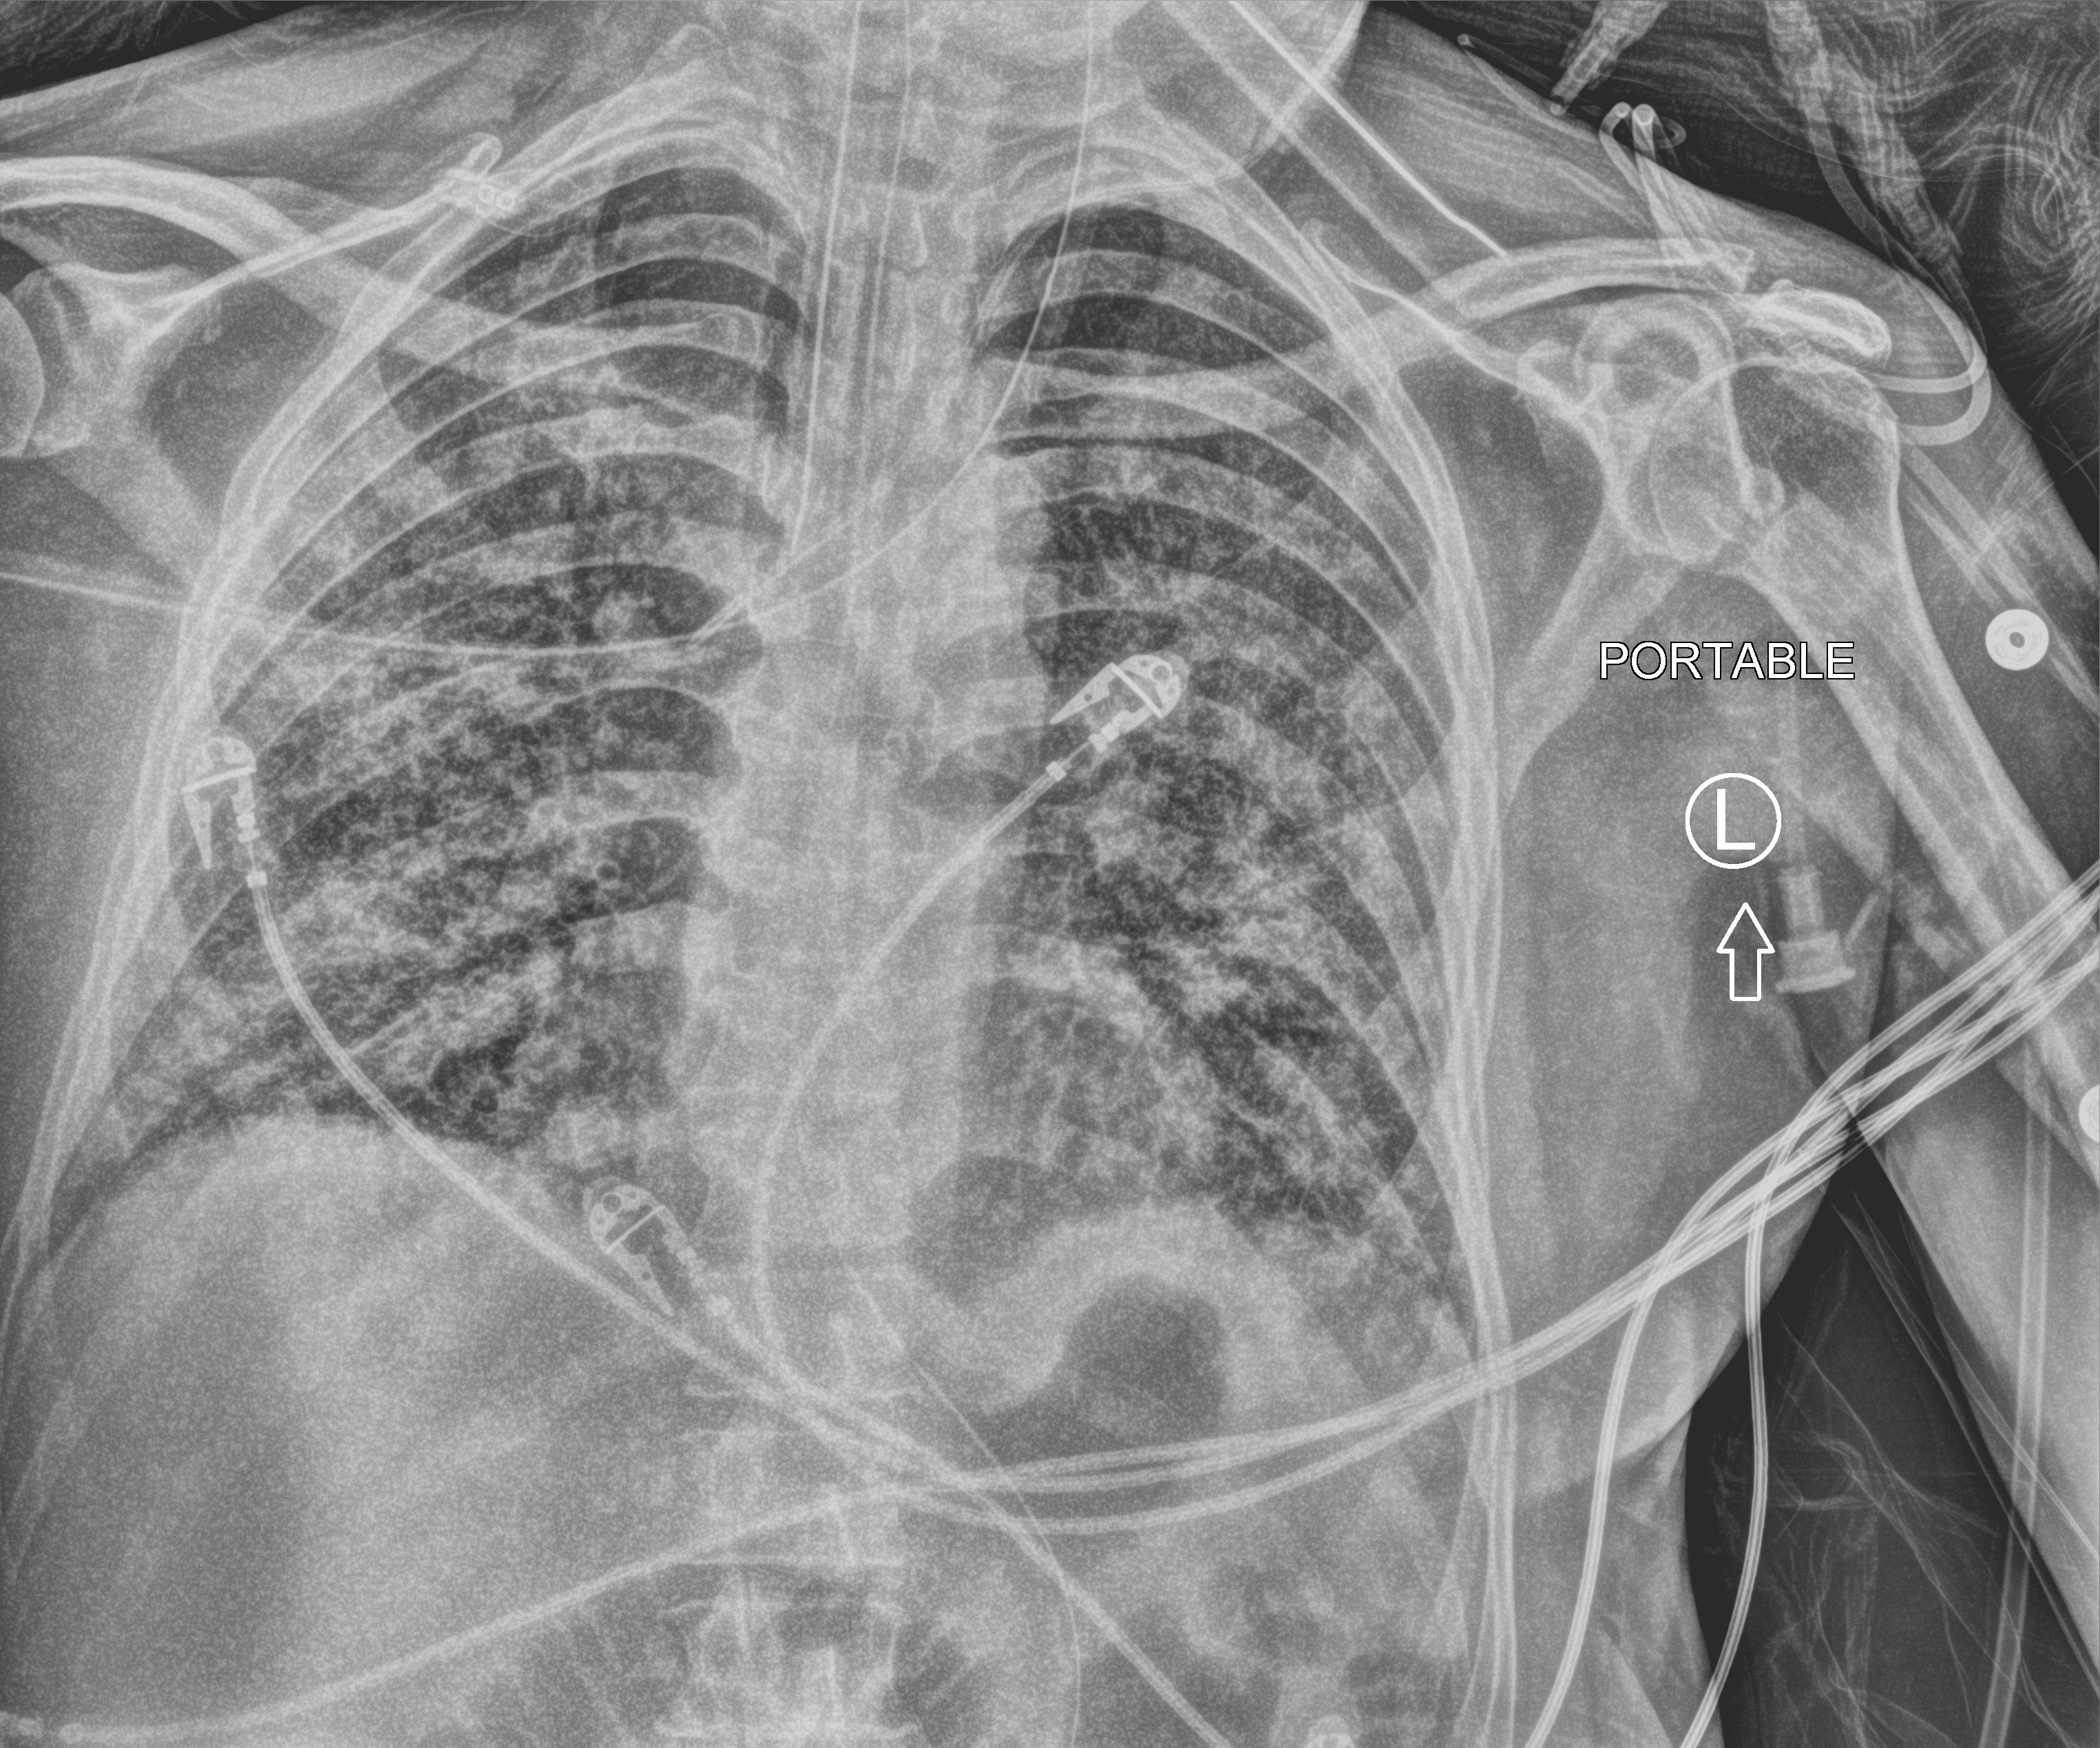
Chest X-ray (portable); anteroposterior (AP) projection. Male patient hospitalised with COVID-19, age 60–74 years.
Admission-level facts for this patient (not findings on this image; timing relative to this image not recorded): admitted to intensive care during this hospital stay: yes.